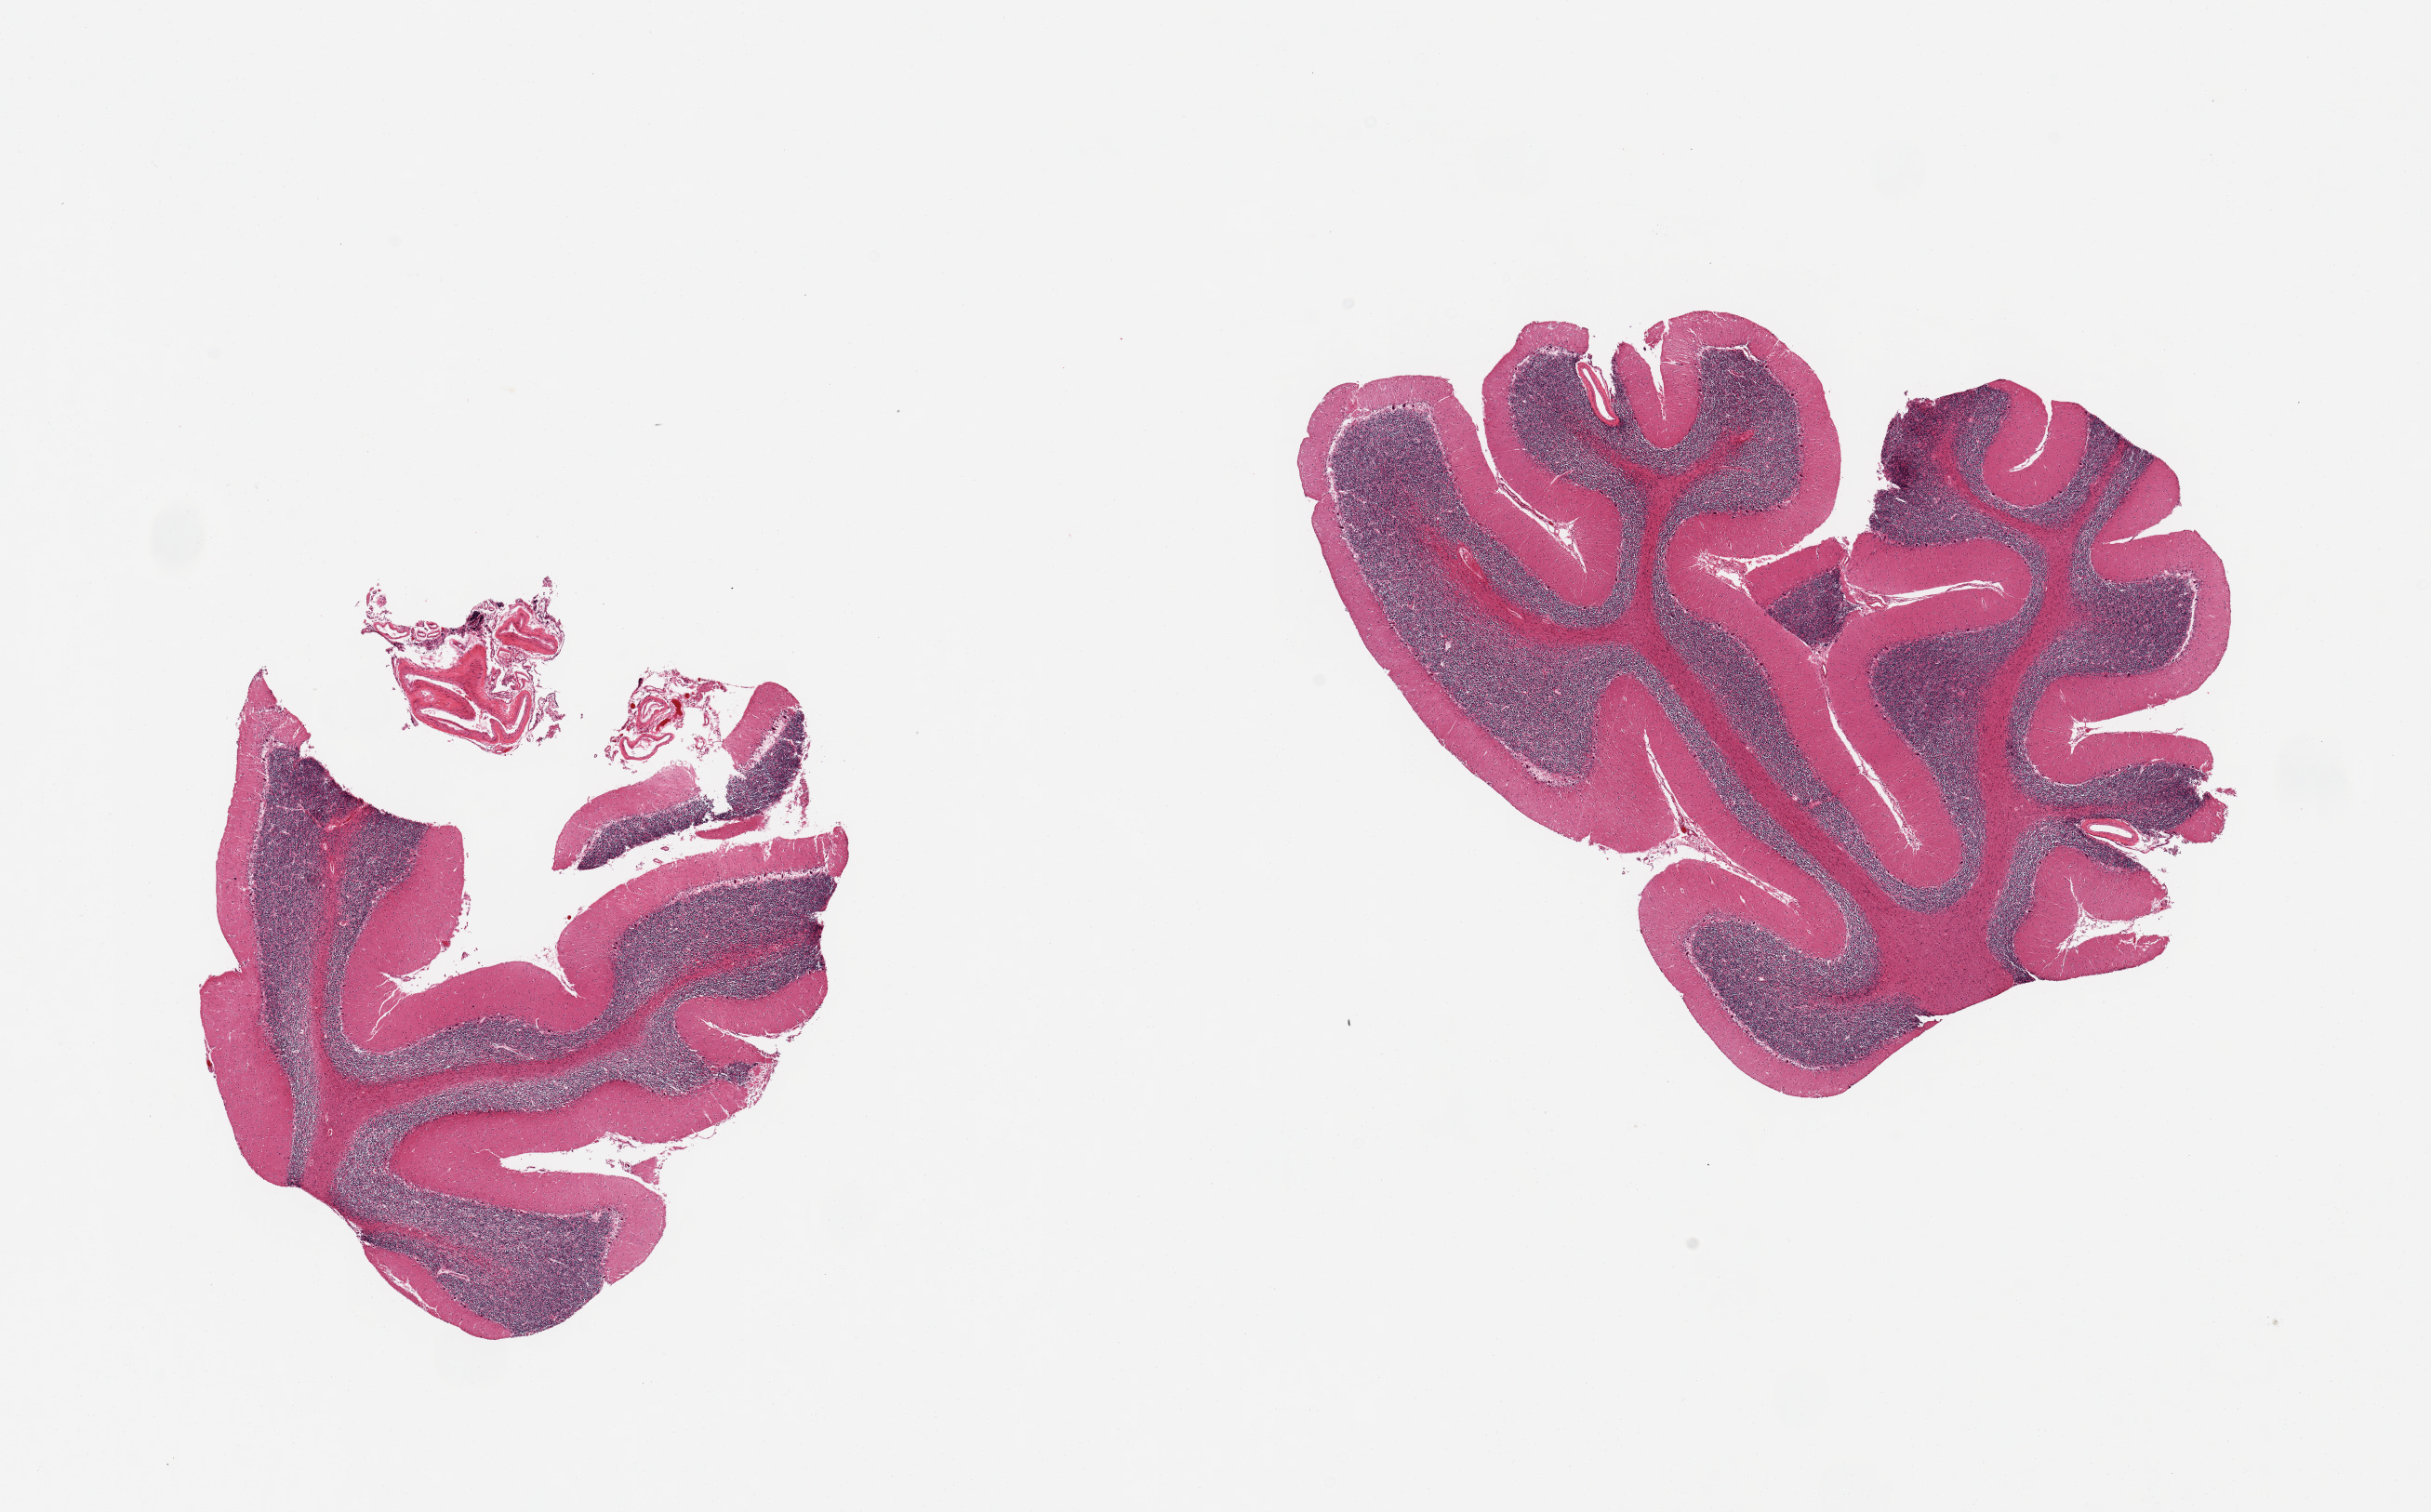
Digitized H&E-stained section, brightfield — shown as a low-resolution overview of the whole scanned area (about 20.7 x 12.9 mm, acquisition: 20x scan). PAXgene-fixed paraffin-embedded (PFPE) section. Target tissue: cerebellum. Tissue donor sample.
• review note (as recorded): 2 pieces